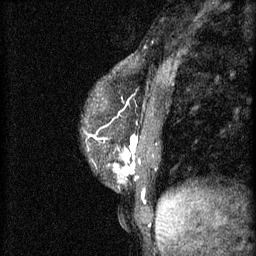
Breast MRI (dynamic contrast-enhanced), one sagittal slice; slice 20 of 60 in the series (ordered by position); 3 images stored at this slice position (order not interpretable as contrast timing); 1.5 T; TE 4.2 ms, TR 11 ms; 2 mm slice thickness; 256 × 256 image matrix, field of view 180 × 180 mm. Female patient, age 37 years.
Annotated regions visible in this slice (semi-automatically segmented with operator editing):
- analysis volume of interest (the breast-tissue region the enhancement analysis was run in; not a lesion): bounding box <86,118,158,179> (left, top, right, bottom; pixels)
- tumour enhancement mask (voxels above the 70 % enhancement threshold inside the analysis volume of interest): <114,136,138,175>